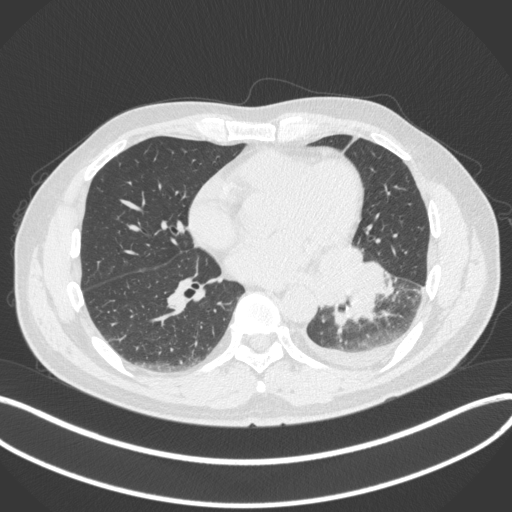
Chest CT, one axial slice. Lung window (W 1500 / L -600 HU). 512 × 512 image matrix, field of view 400 × 400 mm. Male patient, age 58 years. From the clinical record (not read from this slice): clinical TNM (as recorded): T3 N1 M1b; histopathological grade: G3.
Annotated regions visible in this slice (rectangle marked by the reading radiologist):
- lung tumour (recorded histology: small cell carcinoma): bounding box (x1, y1, x2, y2) in pixels: (317, 246, 388, 325)